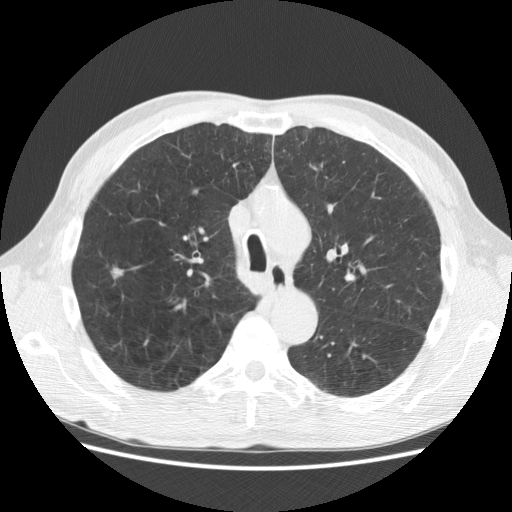
Low-dose screening chest CT, one axial slice. Lung window (W 1500 / L -600 HU). 512 × 512 image matrix, field of view 367 × 367 mm.
Annotated regions visible in this slice (manually delineated by an expert):
- lesion 1 (tumor, upper lobe of right lung): bounding box <113,268,123,277> (left, top, right, bottom; pixels)